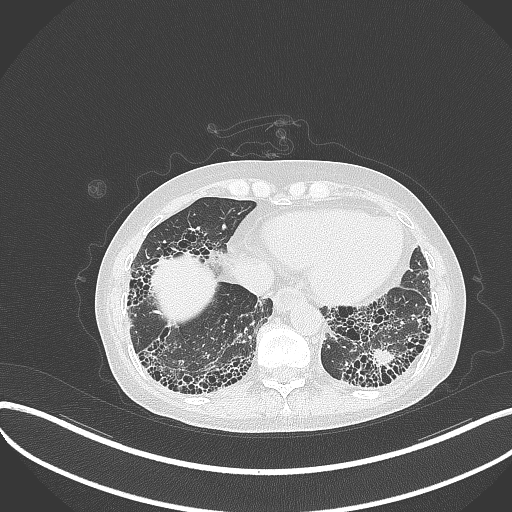
Chest CT, one axial slice; reconstruction kernel B70f; 120 kVp; lung window (W 1500 / L -600 HU); 1 mm slice thickness; 512 × 512 image matrix, field of view 400 × 400 mm. Female patient, age 56 years. Case-level facts recorded for this patient, not image findings: clinical TNM (as recorded): T1 N0 M0.
Structures marked on this image (bounding box drawn by a radiologist):
- lung tumour (recorded histology: adenocarcinoma): bounding box (x1, y1, x2, y2) in pixels: (367, 347, 405, 378)